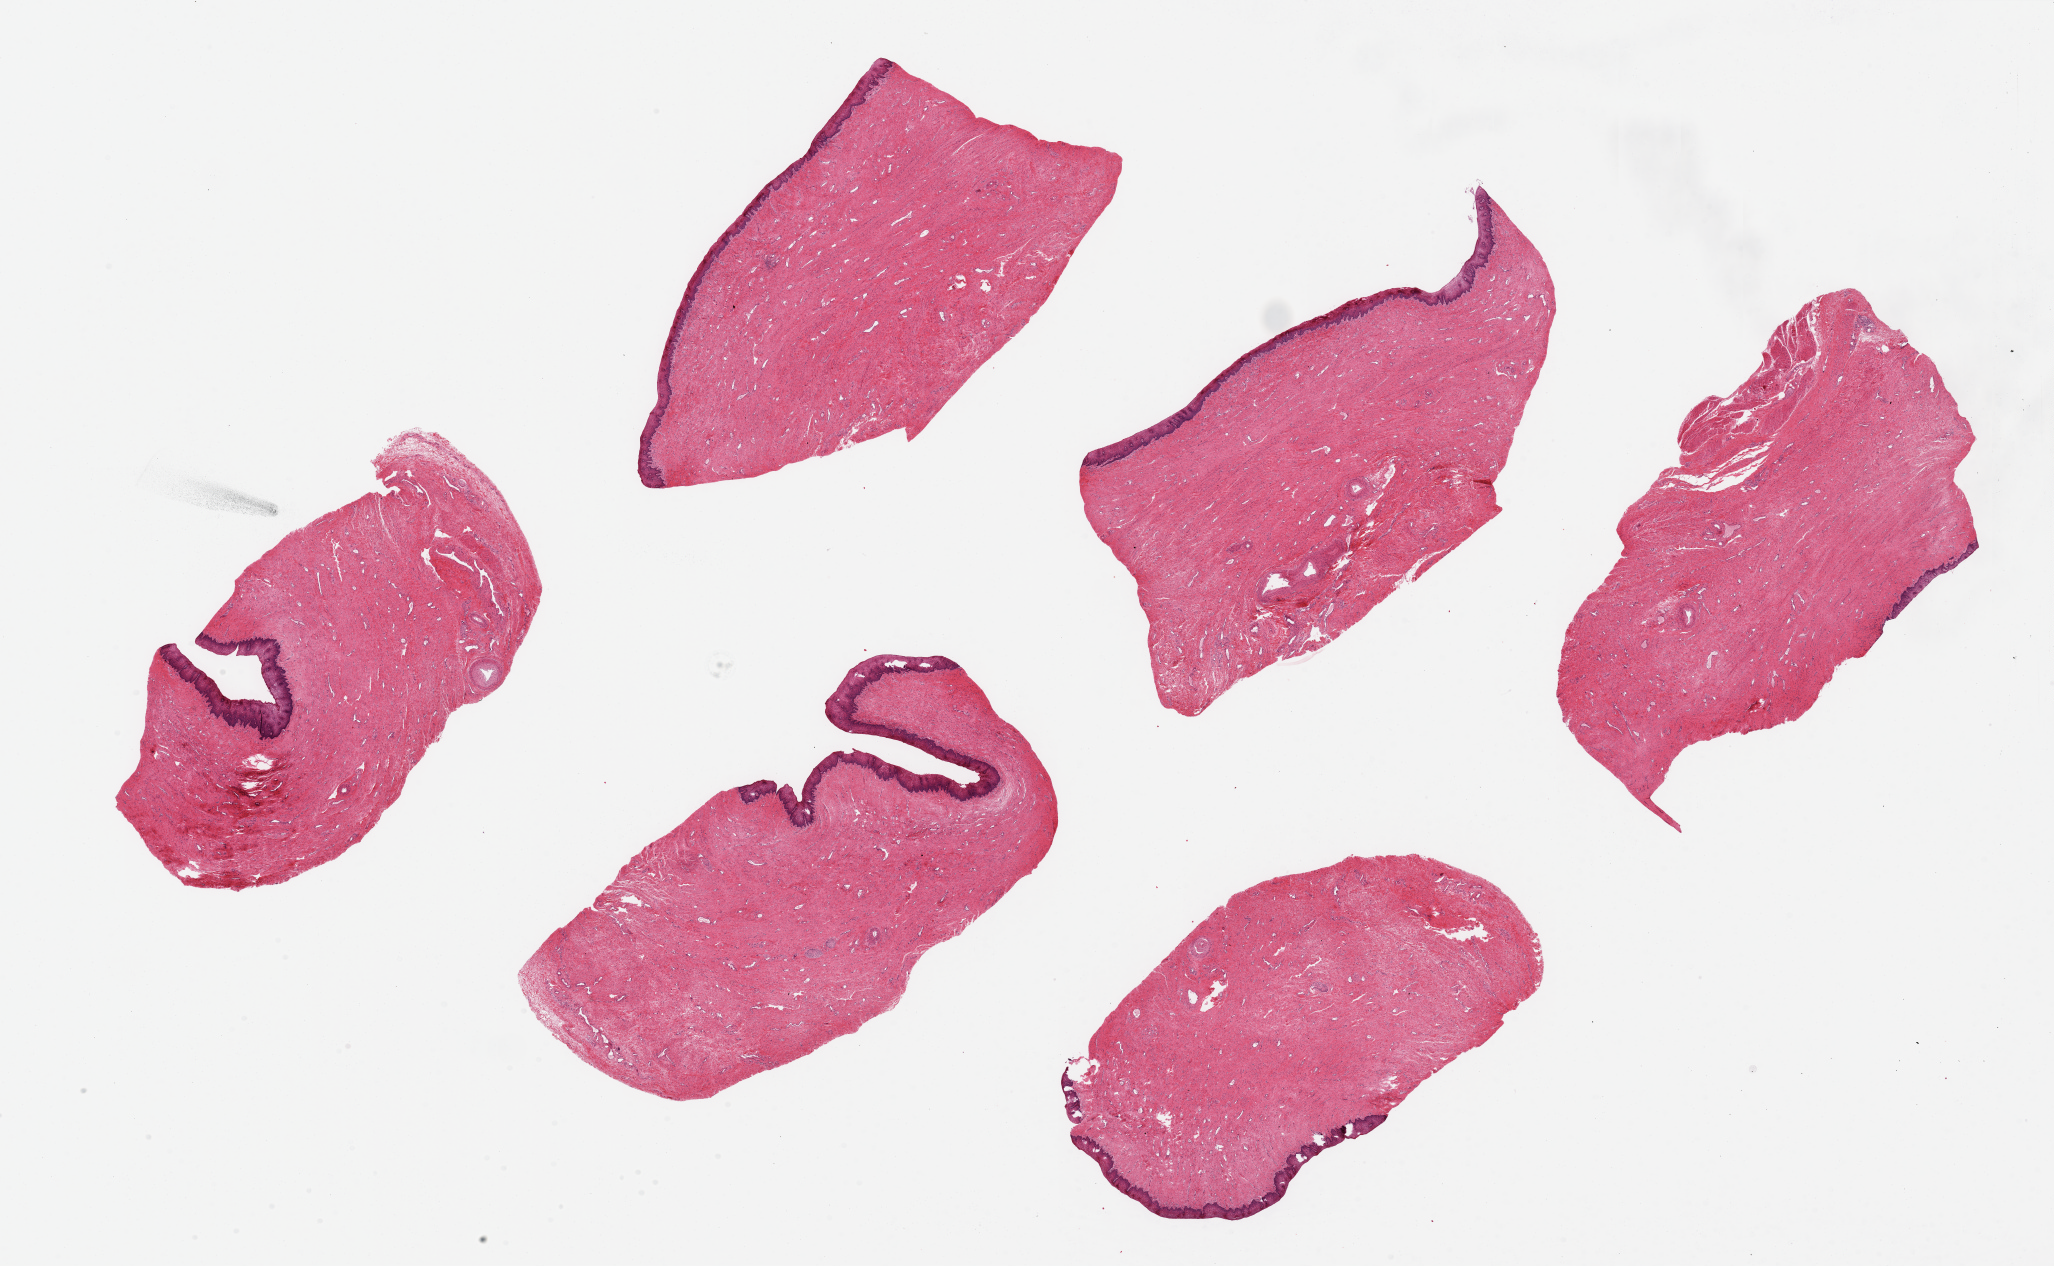
Haematoxylin and eosin whole-slide image, brightfield — a low-resolution overview of the entire scanned area, about 32.5 x 20.0 mm, PAXgene-fixed, paraffin-embedded tissue, sampled site (target tissue): vagina, donor tissue sample. Donor sex: female.
• review note (as recorded): 6 pieces up to 8x4 mm; well preserved